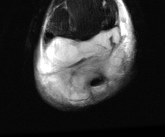
MRI of an extremity soft-tissue mass, one axial slice. Position 14 of 81 along the scan axis. T2-weighted fat-saturated. MR volume resampled by the dataset authors to the PET/CT grid (not the native acquisition matrix). 3.27 mm slice thickness. 165 × 137 image matrix, field of view 161 × 134 mm. Male patient. Case-level facts recorded for this patient, not image findings: histological type: liposarcoma - round cell; grade: high; site of the primary tumour: right calf.
Structures marked on this image (expert contour drawn on MRI and transferred to this co-registered scan by the dataset authors):
- gross tumour volume (mass): box from (x=39, y=27) to (x=127, y=103) px